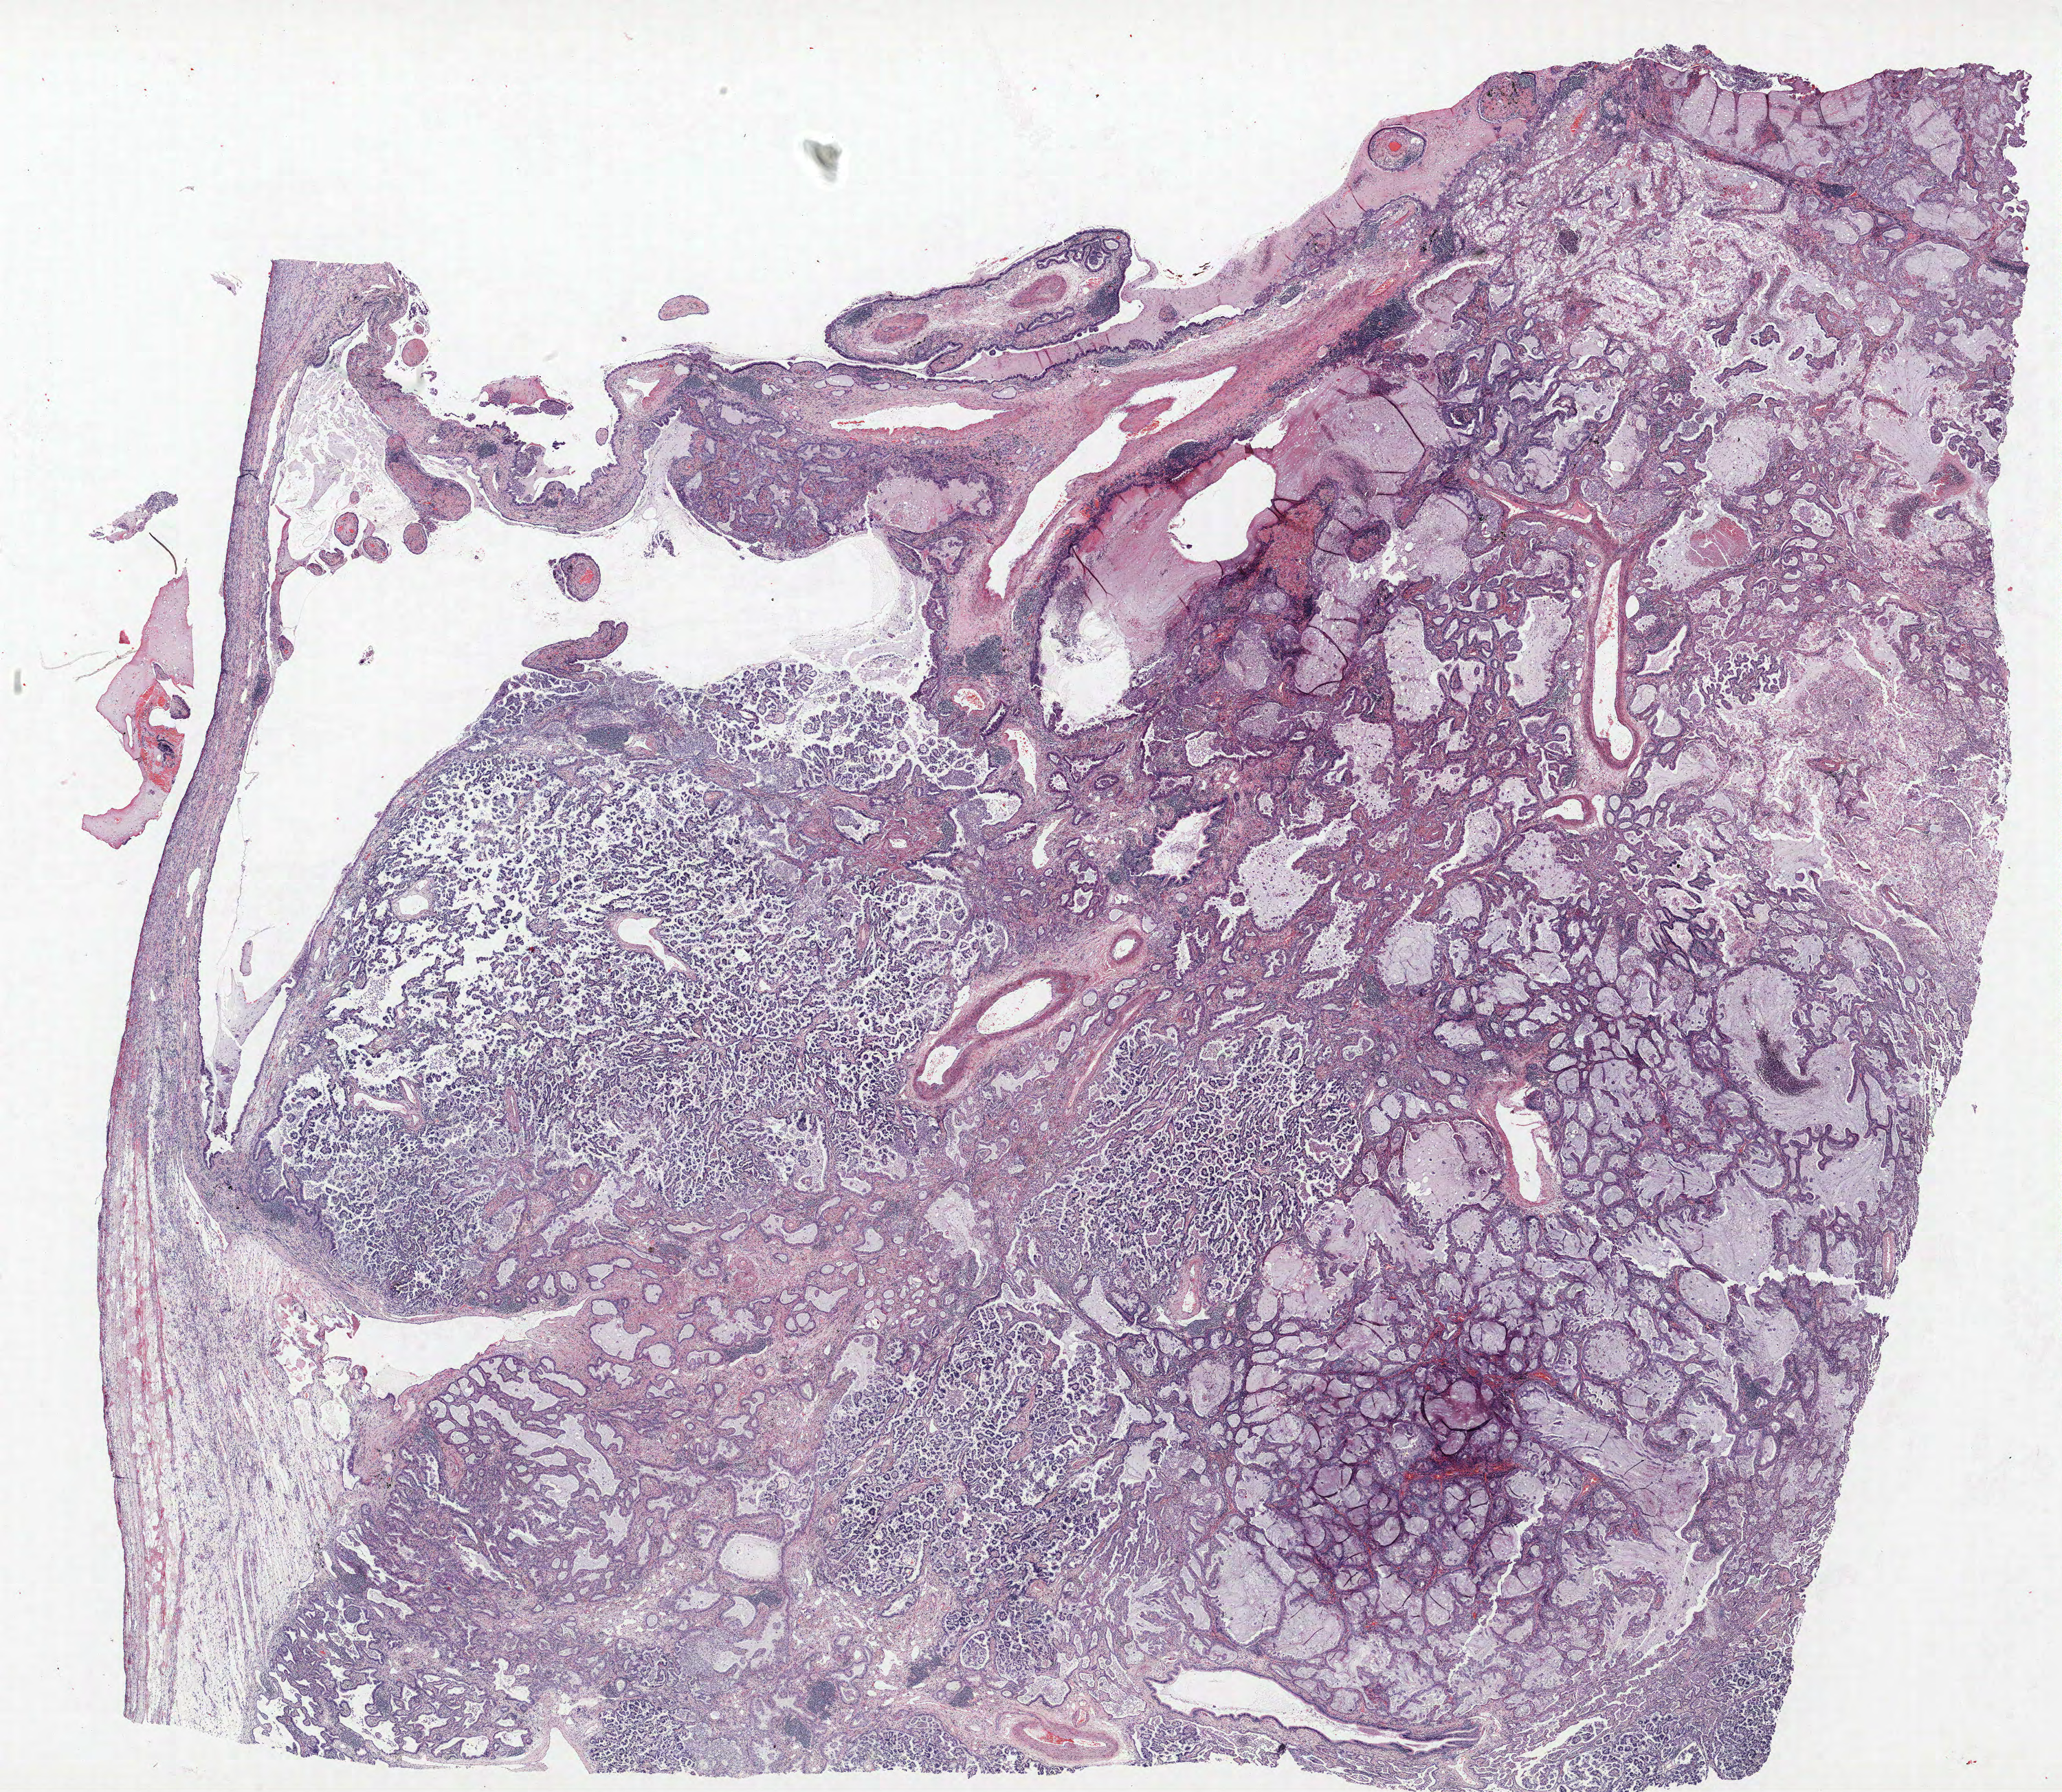
Whole-slide histology image, Hematoxylin and eosin (H&E) stained — shown as a low-resolution overview of the whole scanned area (about 24.0 x 20.9 mm, acquisition: 40x scan); formalin-fixed paraffin-embedded (FFPE) section; lung. Female patient, aged 73 at enrolment. Grade: well differentiated (G1).
Stage (AJCC 6th edition): IV. Primary tumour location (clinical record): right lower lobe. Participant's lung-cancer diagnosis: Mucinous adenocarcinoma. Tumour size (pathology): 85 mm.